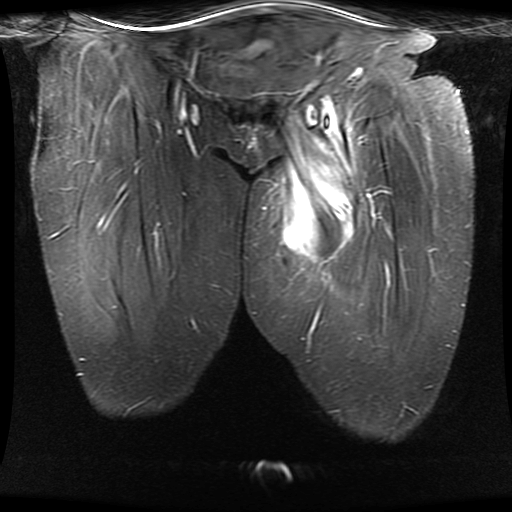
MRI of an extremity soft-tissue mass, one coronal slice. Slice 6 of 30 in the series (ordered by position). STIR. 5 mm slice thickness. 512 × 512 image matrix. Female patient. Case-level facts recorded for this patient, not image findings: histological type: myxofibrosarcoma; grade: intermediate; site of the primary tumour: left thigh.
Outlined on this slice (expert manual segmentation):
- gross tumour volume including surrounding oedema: box from (x=282, y=97) to (x=355, y=263) px
- gross tumour volume (mass): (x=285, y=165)–(x=354, y=259)